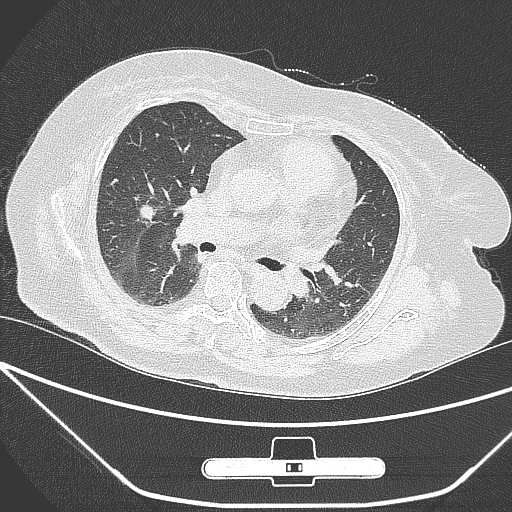
Chest CT, one axial slice. Position 153 of 245 along the scan axis. Lung window (W 1500 / L -600 HU). 1 mm slice thickness. 512 × 512 image matrix, field of view 365 × 365 mm. Female patient, age 65 years. Case-level facts recorded for this patient, not image findings: clinical TNM (as recorded): T1c N0 M0.
Outlined on this slice (bounding box drawn by a radiologist):
- lung tumour (recorded histology: adenocarcinoma): bounding box [x1, y1, x2, y2] px = [134, 198, 165, 233]